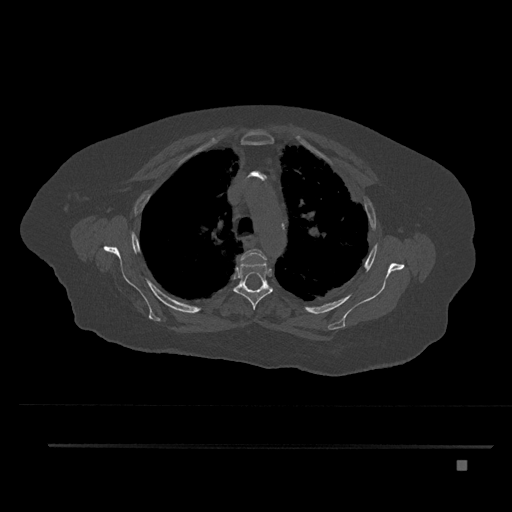
CT including the spine, one axial slice. Position 605 of 797 along the scan axis. Reconstruction kernel Br40s/3. 120 kVp. Bone window (W 1800 / L 400 HU). 0.5 mm slice thickness. 512 × 512 image matrix, field of view 437 × 437 mm. Patient: female, 76 years. From the clinical record (not read from this slice): primary cancer: lung; vertebrae with lytic lesions (as recorded): T11, L3.
Structures marked on this image (semi-automatically segmented with operator editing):
- T3 vertebra: bounding box (x1, y1, x2, y2) in pixels: (241, 248, 267, 263)
- T4 vertebra: (233, 256, 274, 310)